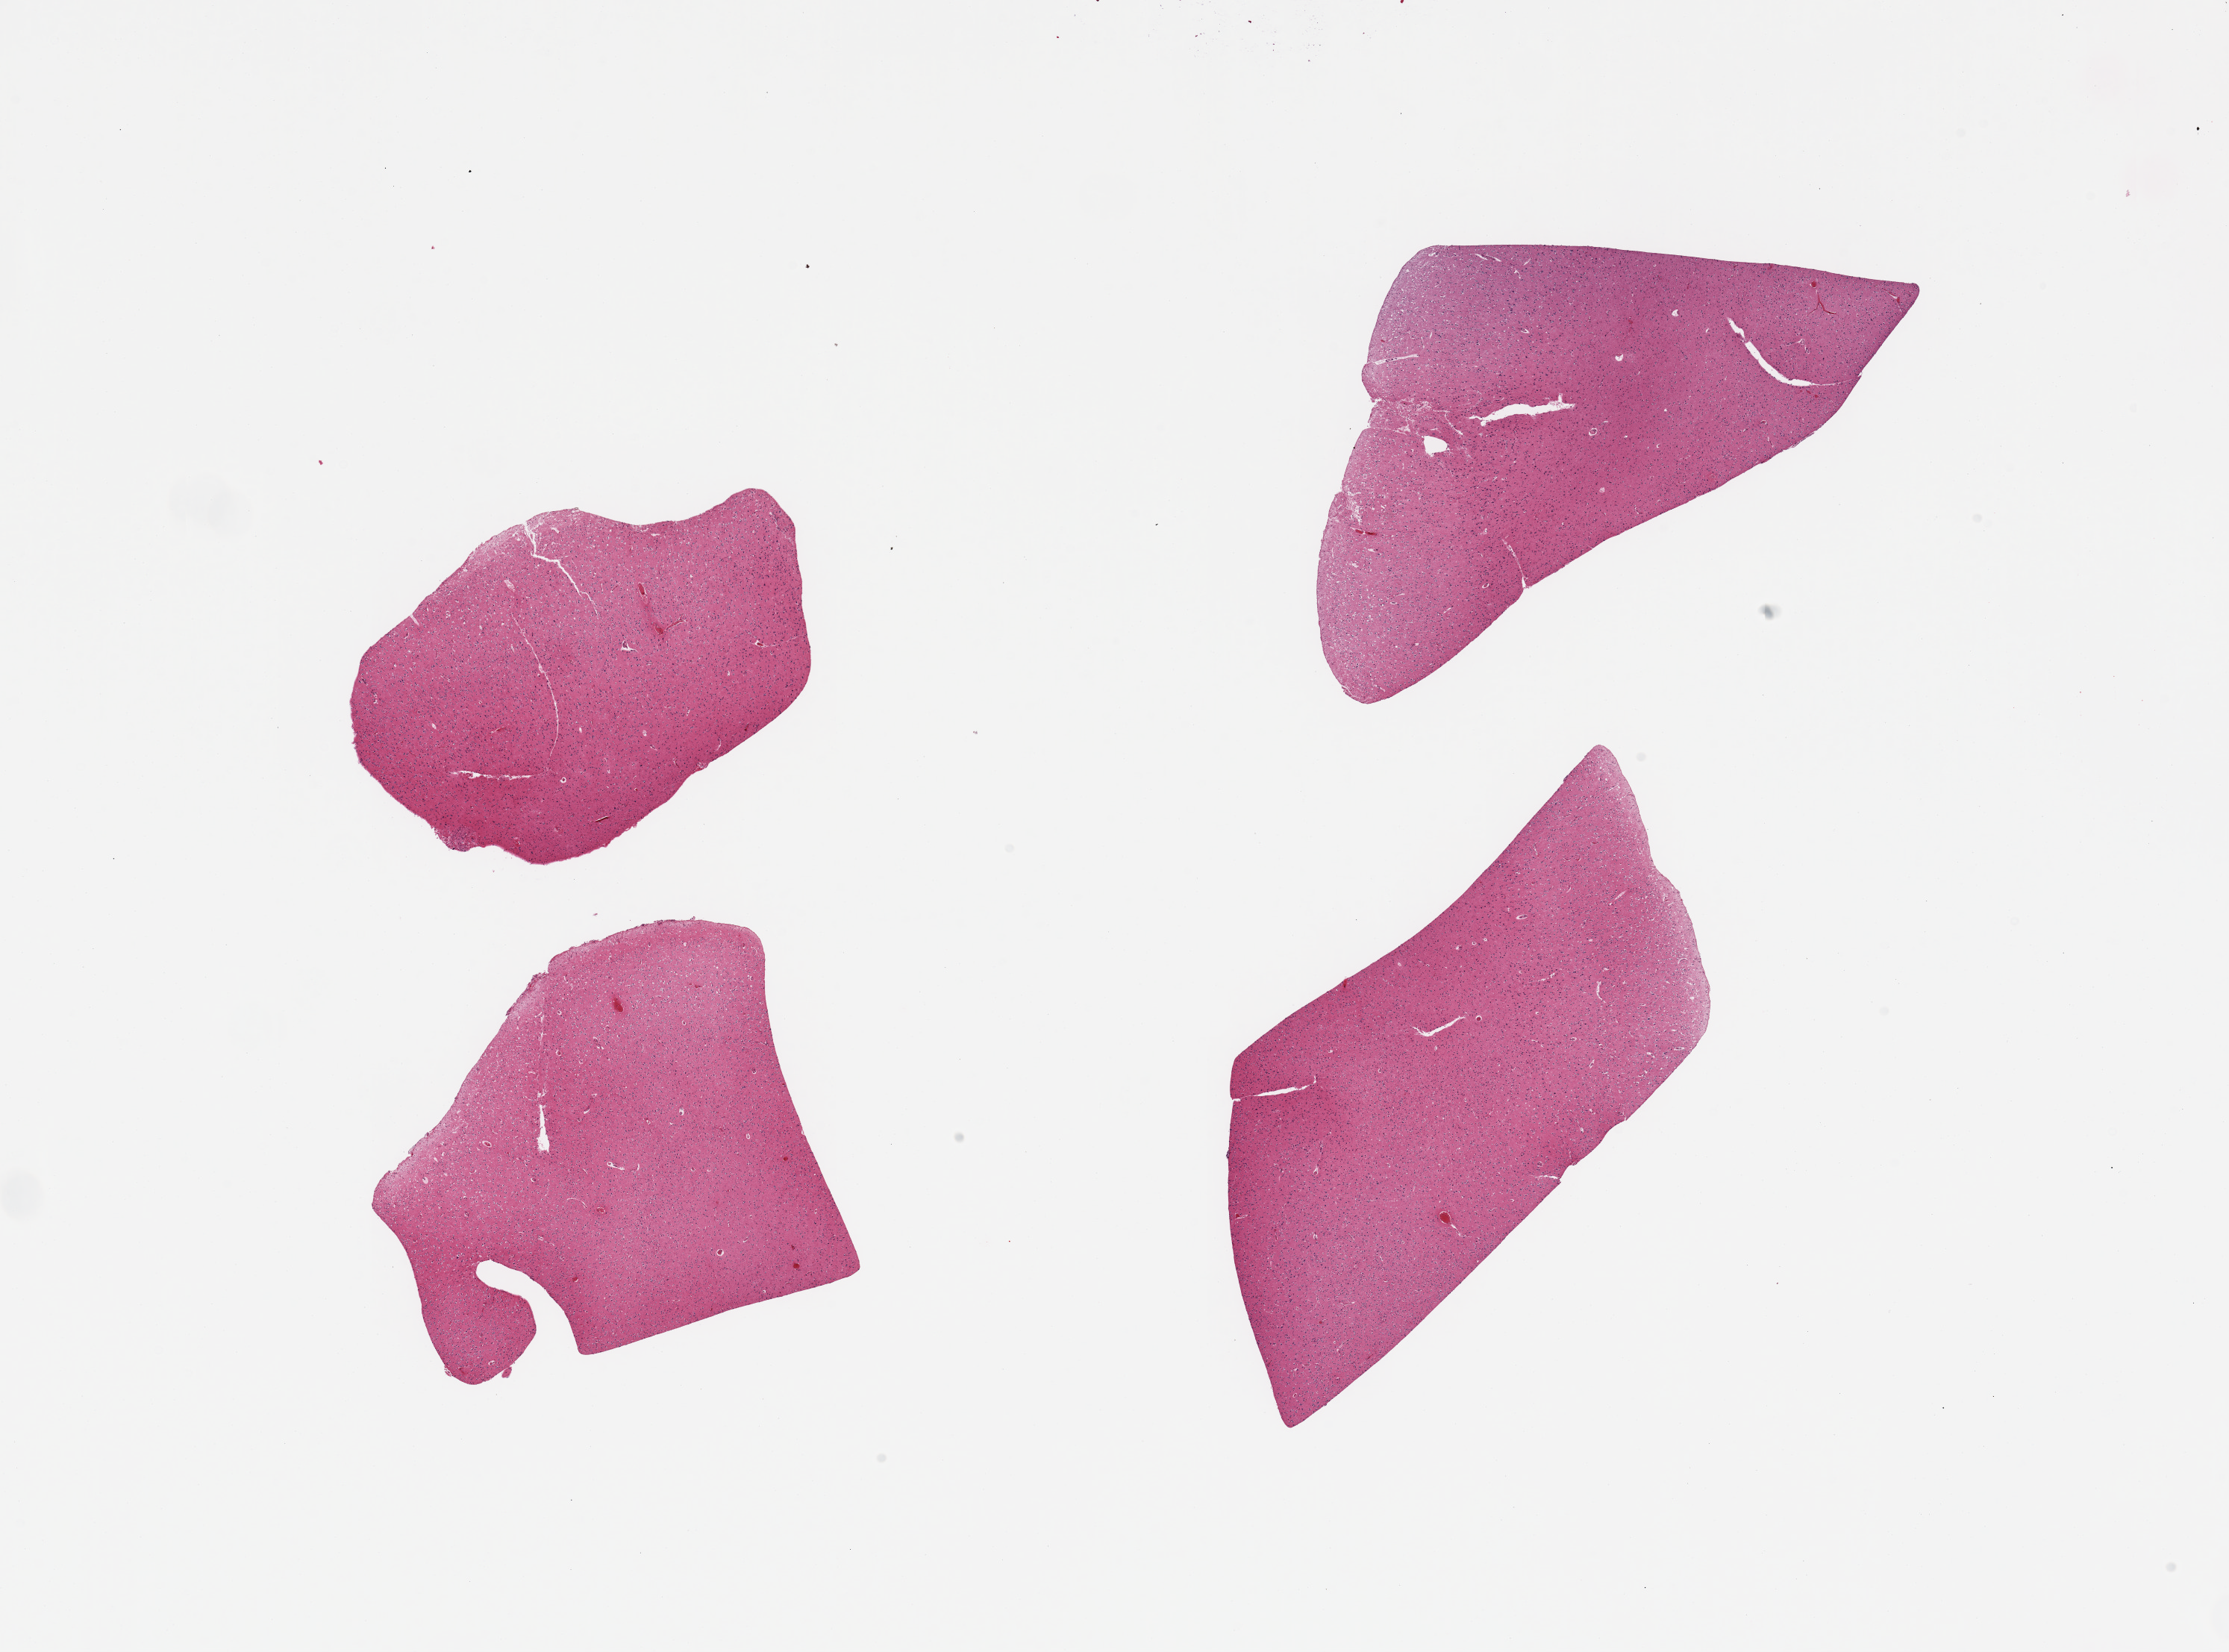
Whole-slide image, H&E stain — whole scanned area (about 23.6 x 17.5 mm, from a 20x scan) shown as a low-resolution overview, PAXgene-fixed paraffin-embedded (PFPE) section, section of cerebral cortex (target tissue), tissue donor sample. Donor sex: female.
Review note (as recorded): 4 pieces, no abnormalities.